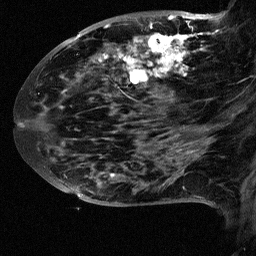
Breast MRI (dynamic contrast-enhanced), one sagittal slice; slice 29 of 64 in the series (ordered by position); dynamic contrast-enhanced study with each time point stored as its own series, time point 2 of 3 at this slice position (early post-contrast, ordered by acquisition time); 1.5 T; TE 4.5 ms, TR 11 ms; 256 × 256 image matrix, field of view 200 × 200 mm. Female patient, age 38 years. From the clinical record (not read from this slice): setting: breast cancer imaged before/during neoadjuvant chemotherapy; receptor status: HR-positive, HER2-negative.
Structures marked on this image (semi-automatic segmentation, software-assisted and operator-edited):
- analysis volume of interest (the breast-tissue region the enhancement analysis was run in; not a lesion): bounding box (x1, y1, x2, y2) in pixels: (88, 18, 252, 126)
- tumour enhancement mask (voxels above the 90 % enhancement threshold inside the analysis volume of interest): (118, 18, 219, 99)